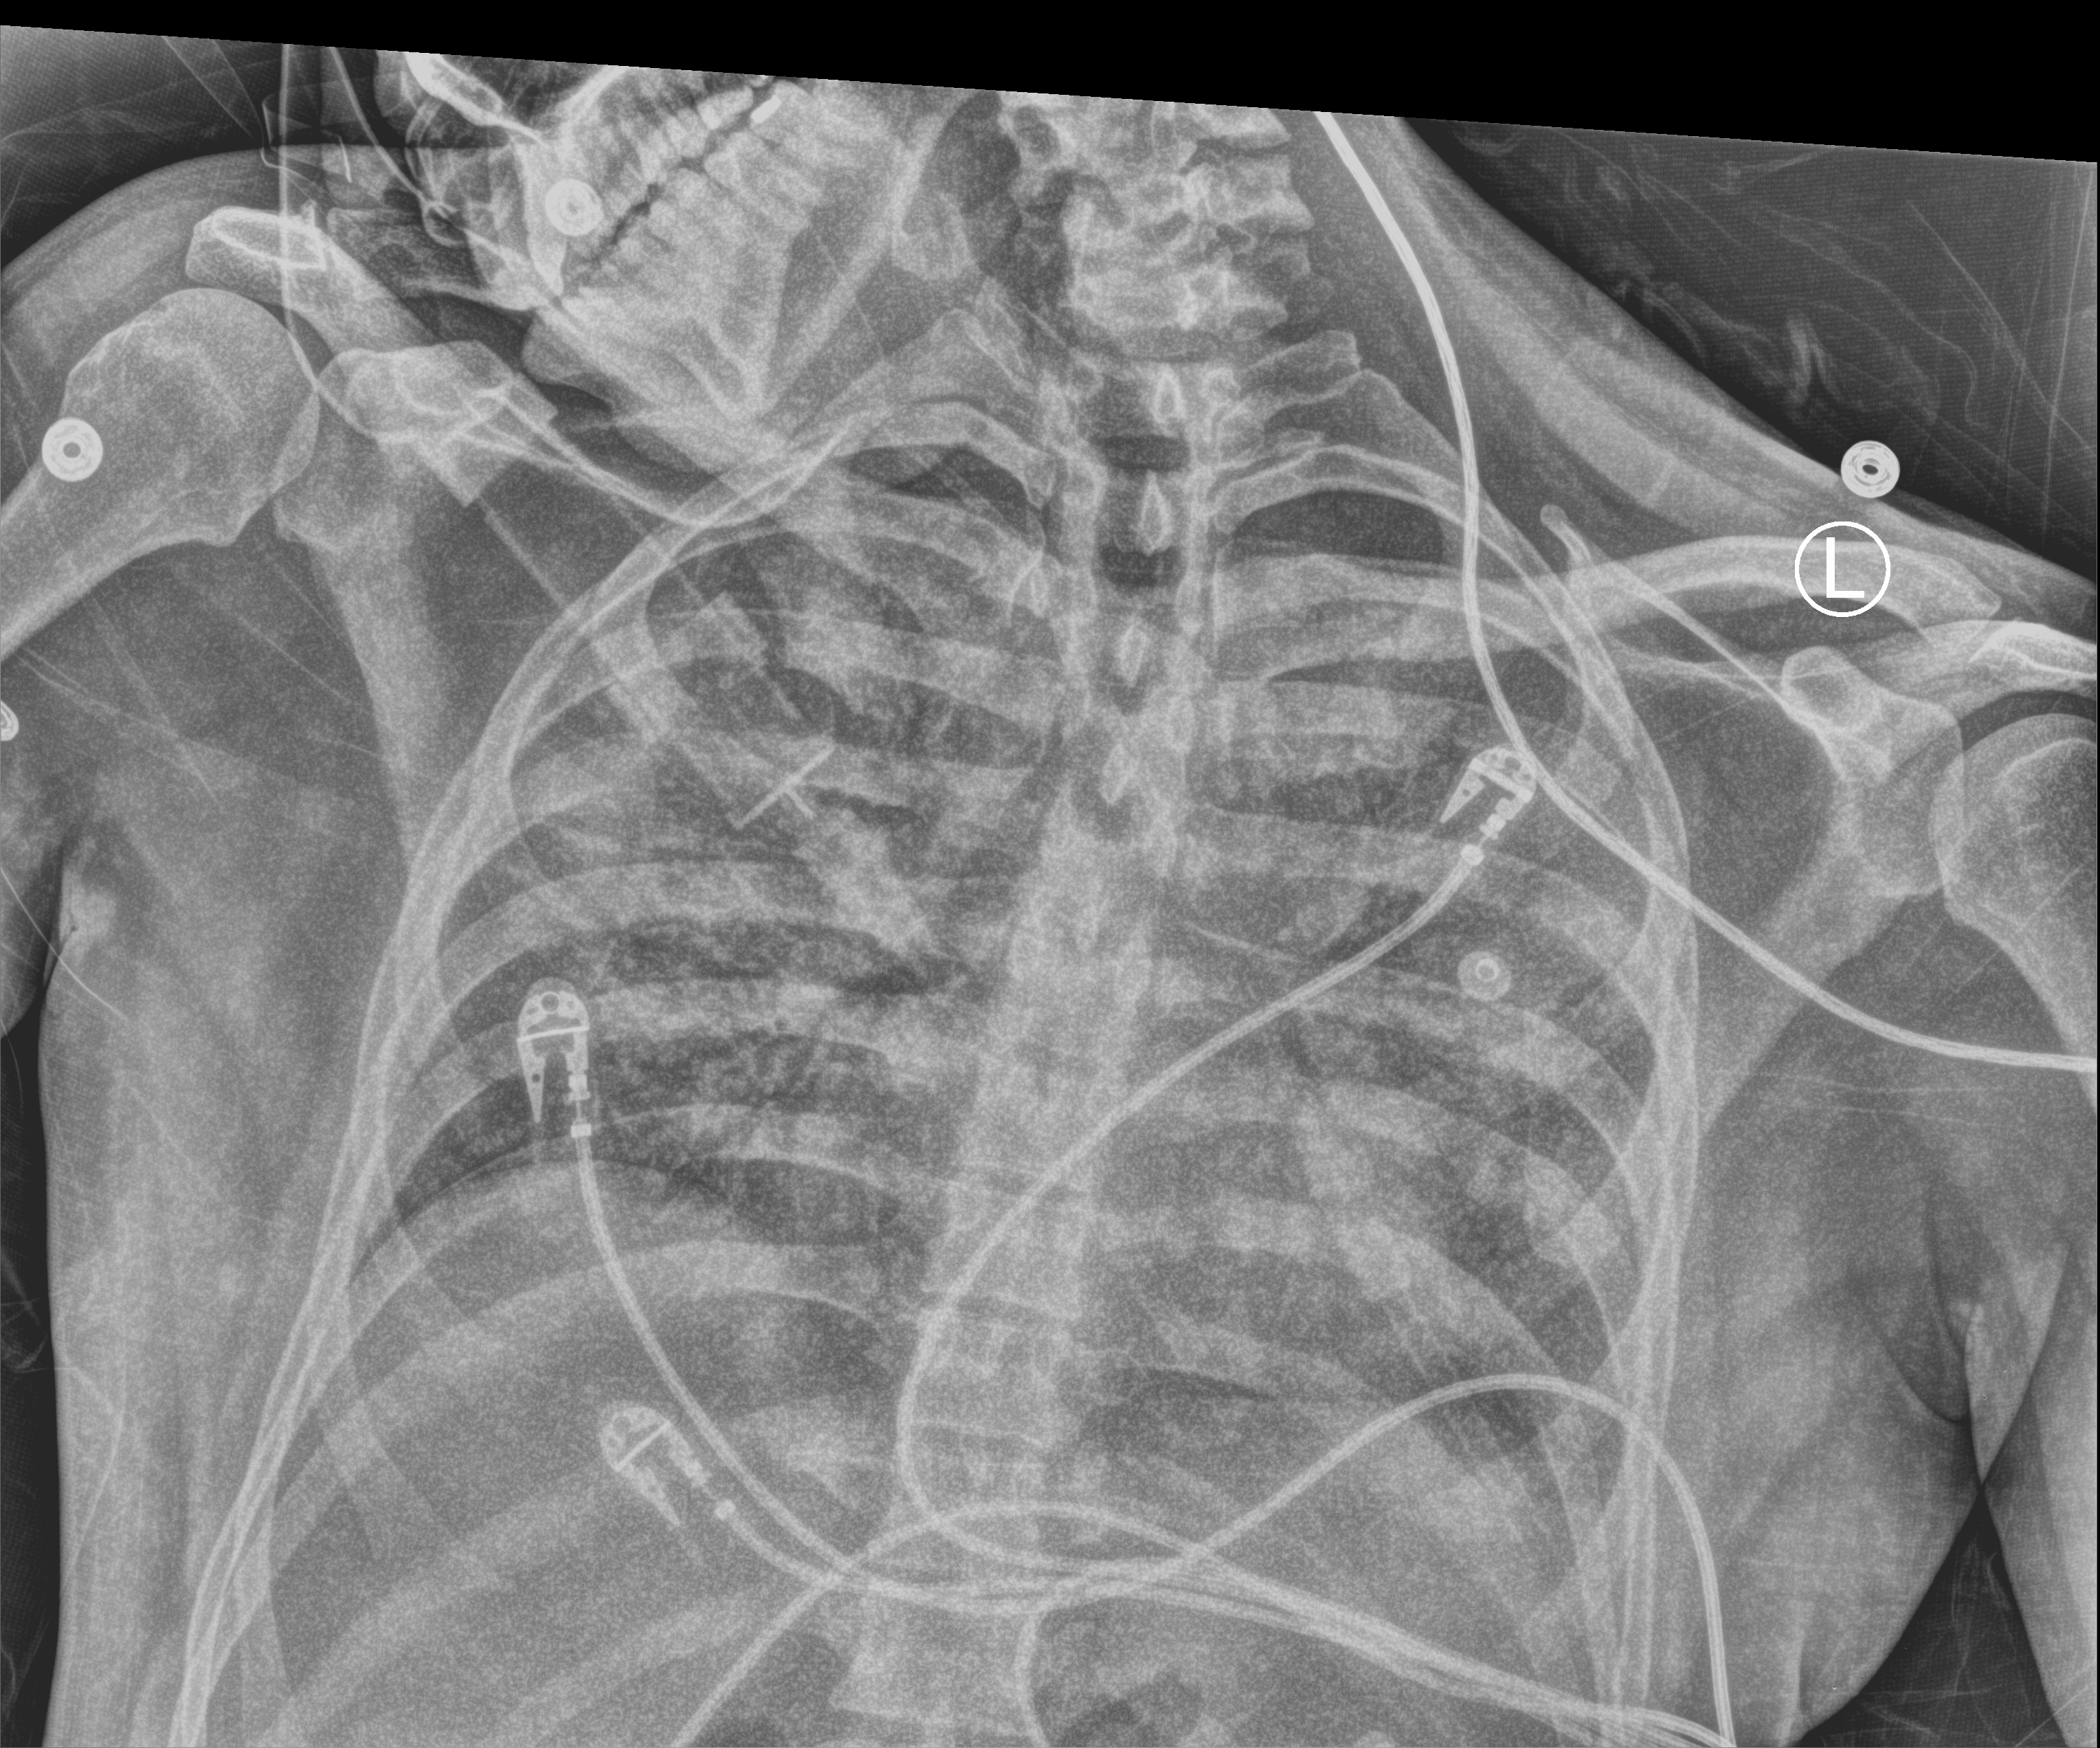
Portable chest radiograph; anteroposterior (AP) projection. Male patient hospitalised with COVID-19, age 18–59 years.
Admission-level facts for this patient (not findings on this image; timing relative to this image not recorded):
- other chronic lung disease (admission record): no
- mechanically ventilated during this hospital stay: yes
- chronic kidney disease (admission record): no